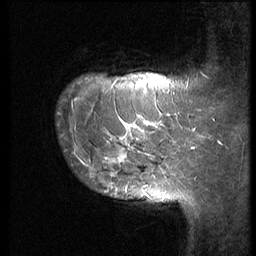
Breast MRI (dynamic contrast-enhanced), one sagittal slice. Position 7 of 62 along the scan axis. 3 images stored at this slice position (order not interpretable as contrast timing). 1.5 T. TE 4.2 ms, TR 9 ms. 2.5 mm slice thickness. 256 × 256 image matrix. Patient: female, 28 years. Case-level facts recorded for this patient, not image findings: setting: breast cancer imaged before/during neoadjuvant chemotherapy.
Structures marked on this image (semi-automatic segmentation, software-assisted and operator-edited):
- analysis volume of interest (the breast-tissue region the enhancement analysis was run in; not a lesion): bounding box <56,90,192,178> (left, top, right, bottom; pixels)
- tumour enhancement mask (voxels above the 140 % enhancement threshold inside the analysis volume of interest): <84,115,156,170>